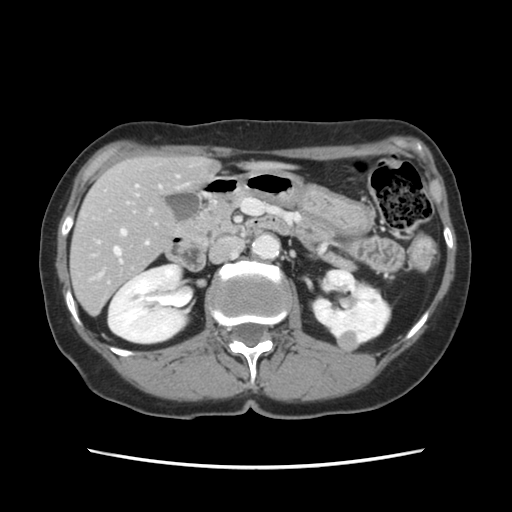
Contrast-enhanced abdominal CT, one axial slice; position 55 of 120 along the scan axis; intravenous contrast given; soft-tissue window (W 400 / L 40 HU); 2.5 mm slice thickness; 512 × 512 image matrix, field of view 330 × 330 mm. Female patient, age 70 years. Case-level facts recorded for this patient, not image findings: diagnosis: colorectal cancer liver metastases, imaged before liver resection; multiple liver metastases: no; largest metastasis: 2.5 cm; disease in both lobes: no.
Structures marked on this image (expert manual segmentation):
- hepatic veins: bounding box [x1, y1, x2, y2] px = [114, 248, 121, 262]
- liver: [71, 157, 216, 313]
- planned liver remnant (the part of the liver to remain after resection): [72, 157, 216, 307]
- portal vein (with intrahepatic branches): [97, 176, 179, 245]